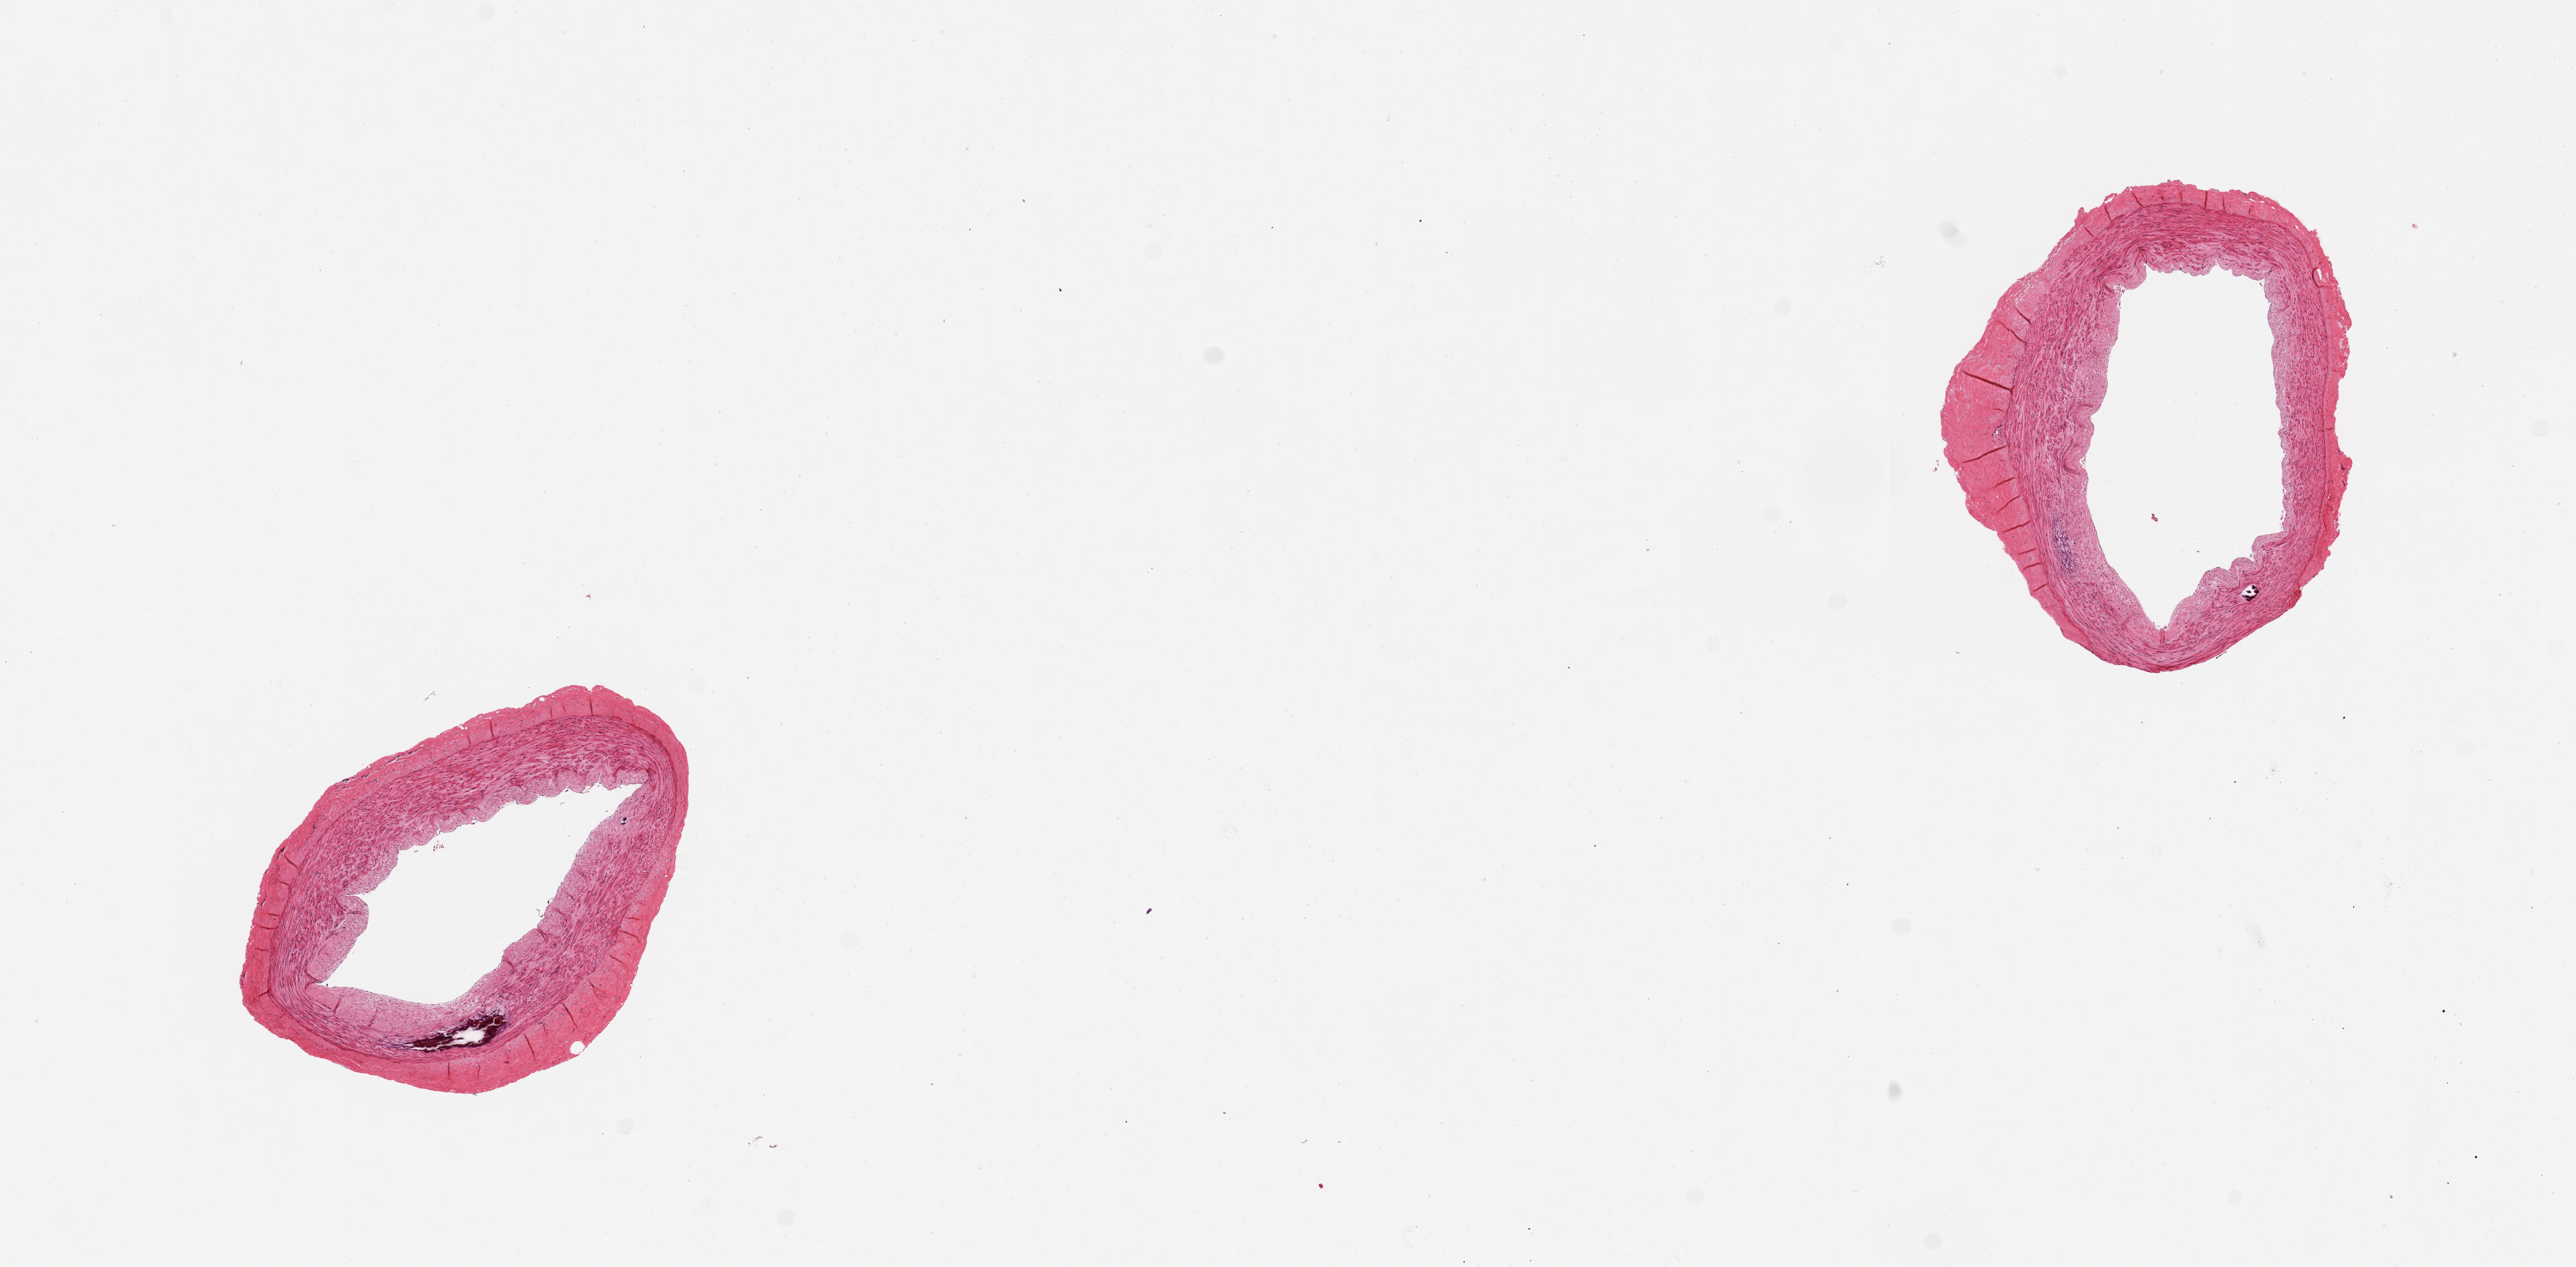
Digitized haematoxylin and eosin-stained section, low-resolution overview of the scanned area, about 14.8 x 7.3 mm (acquisition: 20x scan), PAXgene-fixed paraffin-embedded (PFPE) section, section of tibial artery (target tissue), donor tissue sample. Donor: female.
Pathologist's review note for this sample: 2 pieces; well trimmed; small foci of medial calcification.